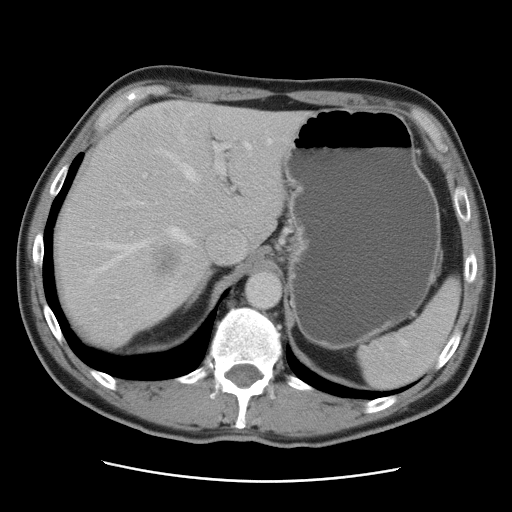
Contrast-enhanced abdominal CT, one axial slice; position 65 of 89 along the scan axis; intravenous contrast given; soft-tissue window (W 400 / L 40 HU); 512 × 512 image matrix, field of view 366 × 366 mm. Male patient, age 59 years. From the clinical record (not read from this slice): diagnosis: colorectal cancer liver metastases, imaged before liver resection; multiple liver metastases: yes; largest metastasis: 0.6 cm; chemotherapy before resection: no.
Annotated regions visible in this slice (expert manual segmentation):
- hepatic veins: bounding box (x1, y1, x2, y2) in pixels: (86, 140, 272, 283)
- liver: (54, 102, 309, 349)
- planned liver remnant (the part of the liver to remain after resection): (99, 101, 301, 248)
- portal vein (with intrahepatic branches): (131, 144, 229, 234)
- liver metastasis: (159, 252, 179, 275)